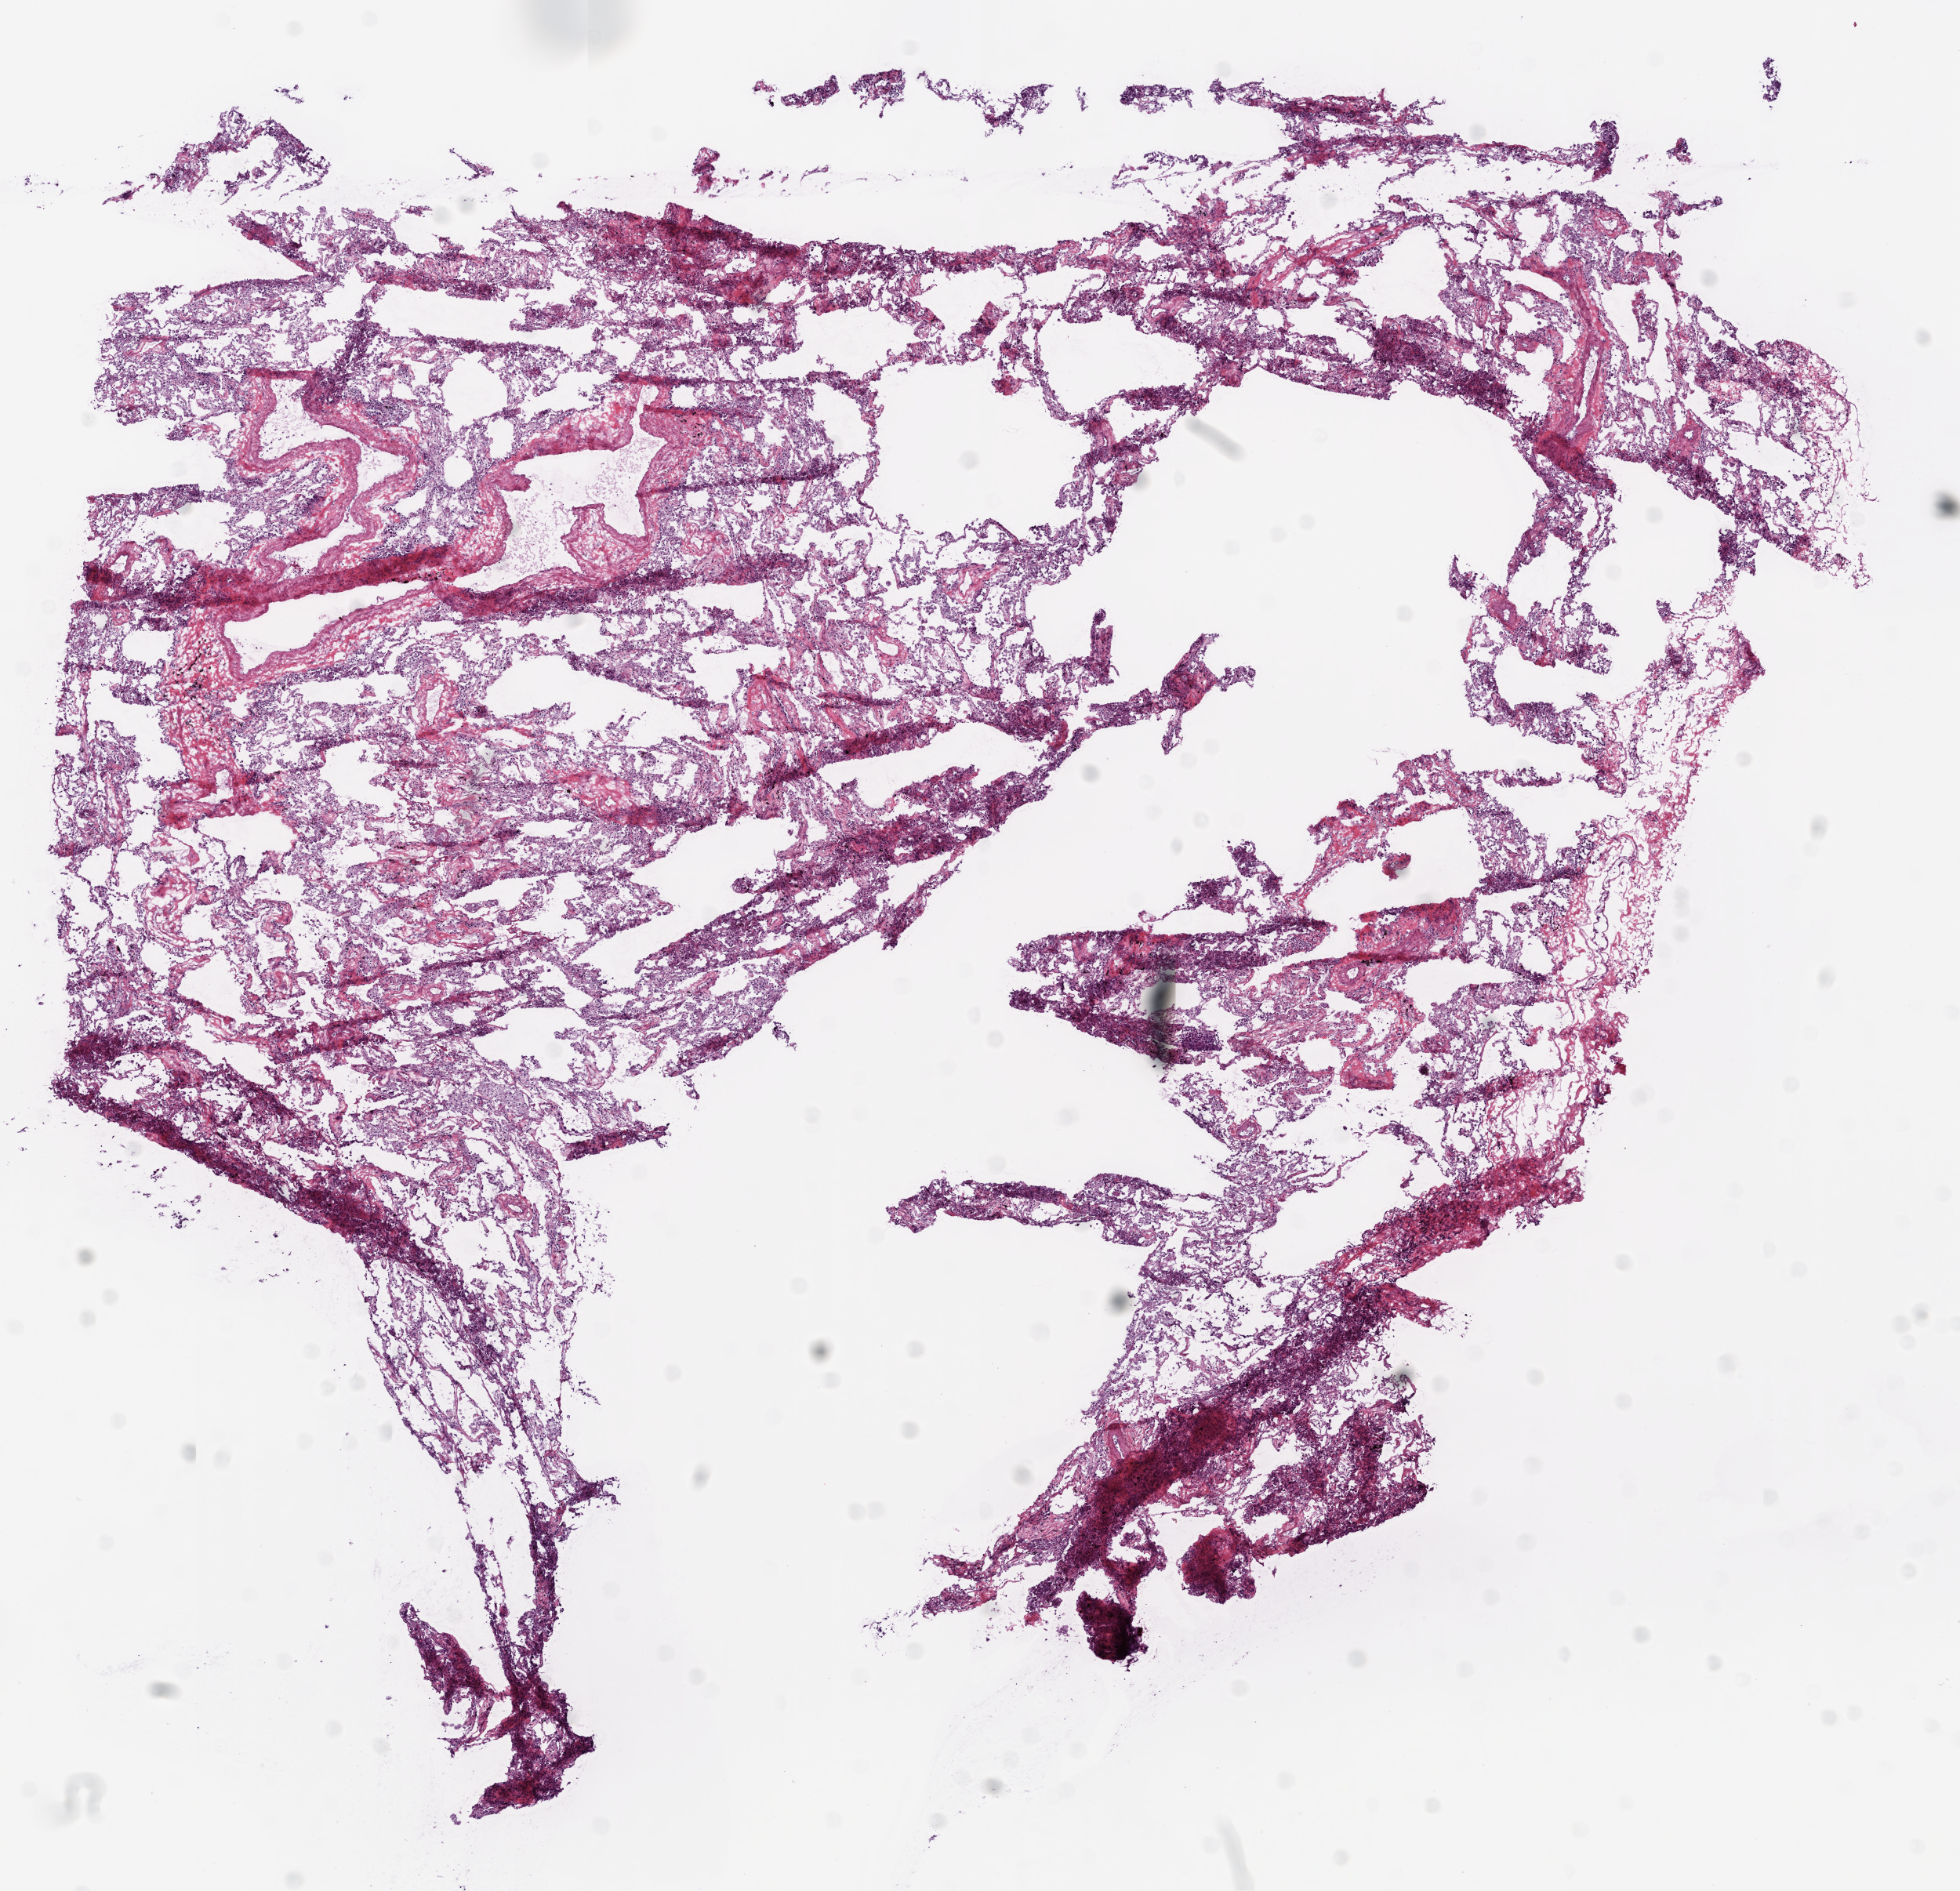
H&E-stained whole-slide image, low-resolution overview of the scanned area, about 10.0 x 9.7 mm. Frozen section. Solid tissue normal (non-tumour tissue) sample from the lung. Male, age 68 years at initial diagnosis.
This section: solid tissue normal sample (biorepository sample class). Patient diagnosis: Squamous cell carcinoma, NOS (upper lobe, lung).